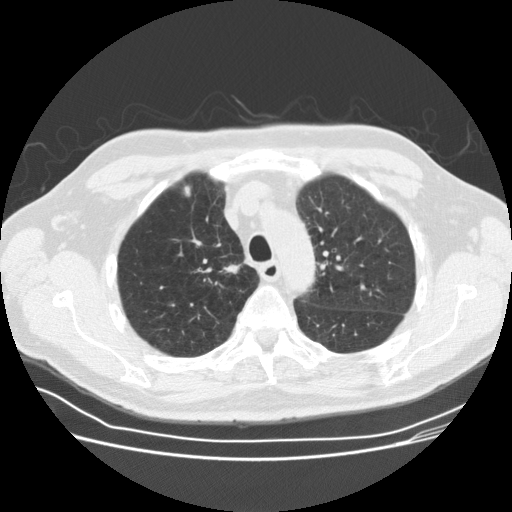
Low-dose screening chest CT, one axial slice; slice 122 of 164 in the series (ordered by position); 120 kVp; lung window (W 1500 / L -600 HU); 512 × 512 image matrix.
Annotated regions visible in this slice (manually delineated by an expert):
- lesion 1 (tumor, upper lobe of right lung): bounding box <223,264,240,274> (left, top, right, bottom; pixels)